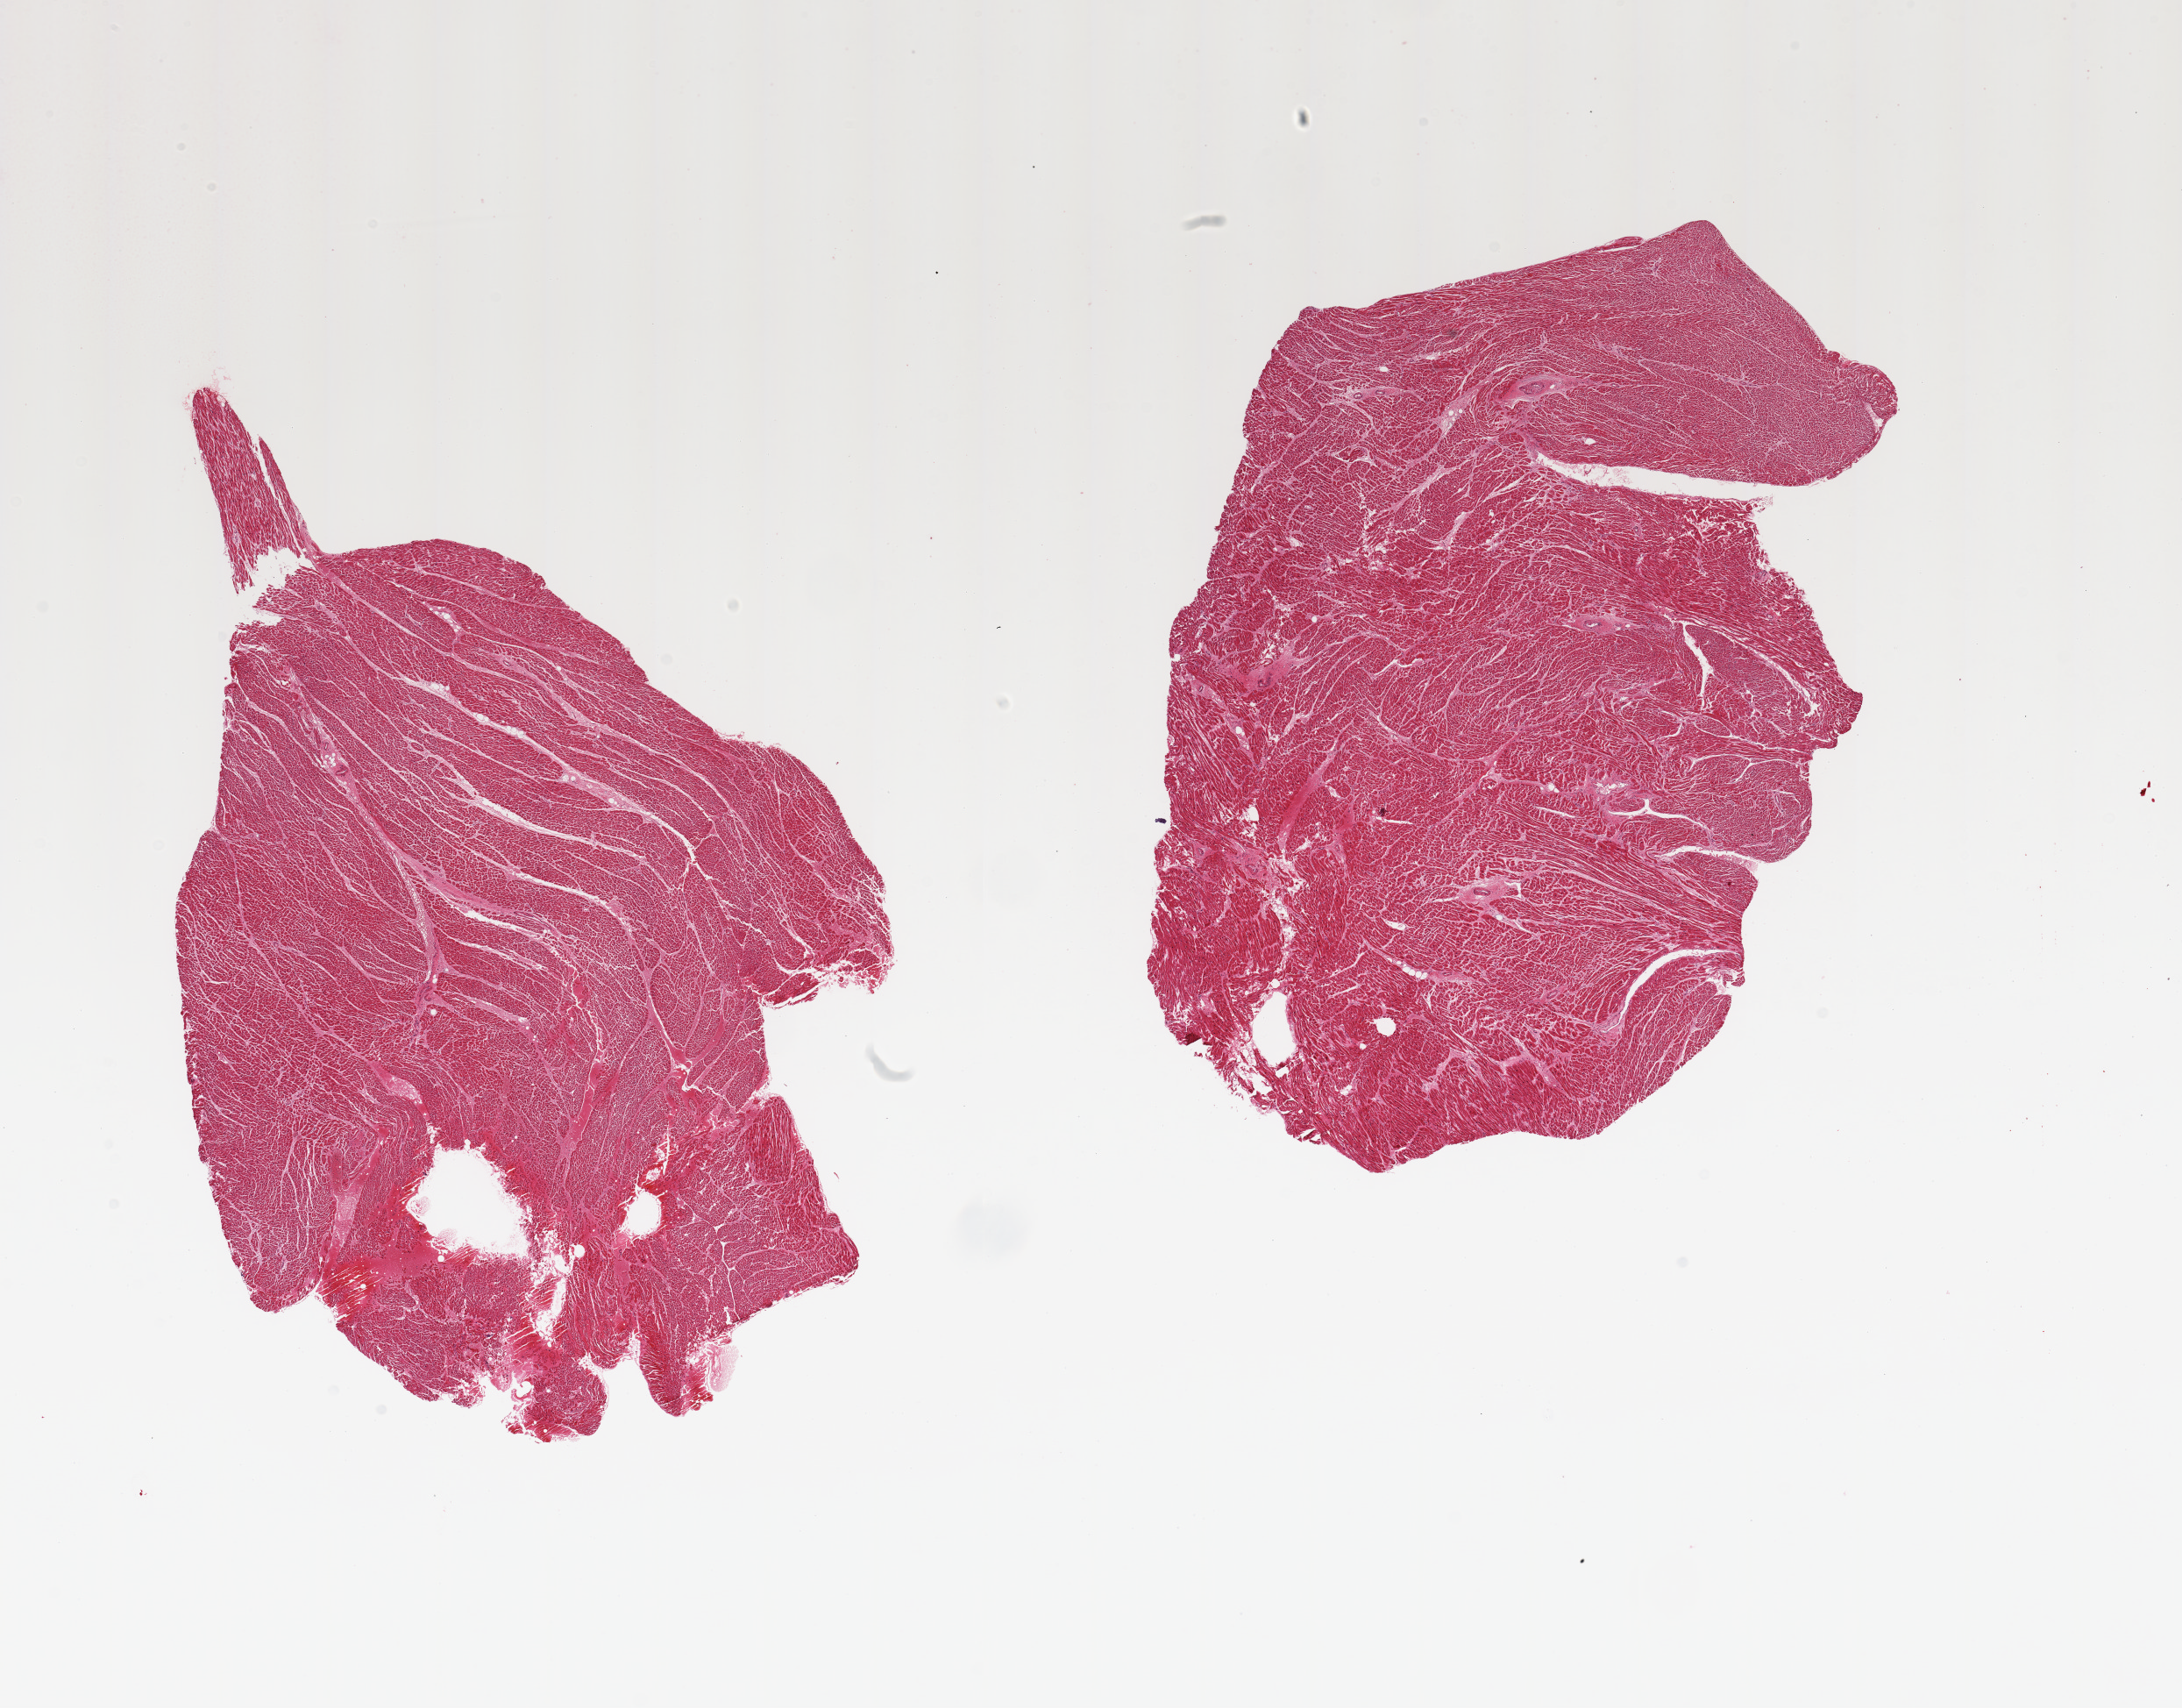
Digitized H&E-stained section, brightfield — a low-resolution overview of the entire scanned area, about 19.7 x 15.4 mm (acquisition: 20x scan). PAXgene-fixed paraffin-embedded (PFPE) section. Sampled site (target tissue): heart. Donor tissue sample. Male donor.
- pathologist's review note for this sample: 2 pieces; ~4 sq mm recent hemorrhage in 1 piece; lesser amount in other piece